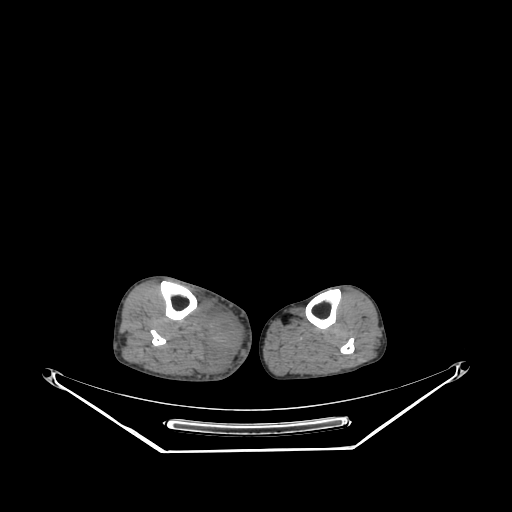
CT of an extremity soft-tissue mass (from a PET/CT study), one axial slice. Slice 128 of 267 in the series (ordered by position). Reconstruction kernel SOFT. 140 kVp. Soft-tissue window (W 400 / L 40 HU). 3.75 mm slice thickness. 512 × 512 image matrix. Male patient. From the clinical record (not read from this slice): histological type: pleiomorphic liposarcoma; grade: high; site of the primary tumour: right calf.
Outlined on this slice (expert contour drawn on MRI and transferred to this co-registered scan by the dataset authors):
- gross tumour volume including surrounding oedema: bounding box [x1, y1, x2, y2] px = [201, 304, 245, 375]
- gross tumour volume (mass): [206, 313, 245, 352]